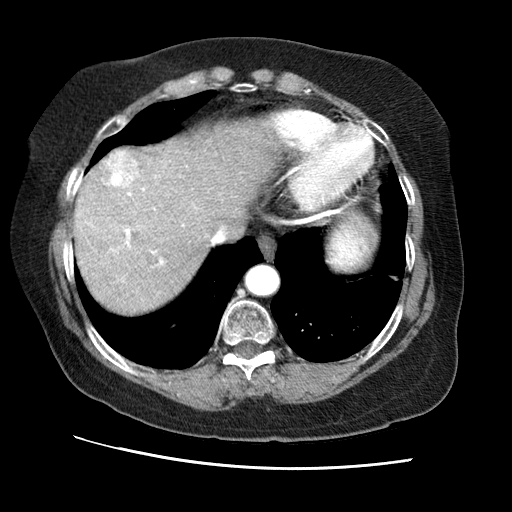
Contrast-enhanced abdominal CT (liver protocol), one axial slice. 120 kVp. Soft-tissue window (W 400 / L 40 HU). 2.5 mm slice thickness. 512 × 512 image matrix. Case-level facts recorded for this patient, not image findings: diagnosis: hepatocellular carcinoma (patient treated with transarterial chemoembolisation; whether this scan precedes or follows treatment is not stated here); TNM stage (as recorded): Stage-II; Child-Pugh class: A.
Outlined on this slice (semi-automatically segmented with operator editing):
- abdominal aorta: box from (x=249, y=267) to (x=278, y=295) px
- liver parenchyma outside the tumour (the mass and vessels are separate outlines, so this box may not span the whole liver): (x=74, y=126)–(x=276, y=313)
- mass: (x=91, y=148)–(x=138, y=188)
- liver vessels: (x=88, y=176)–(x=196, y=265)